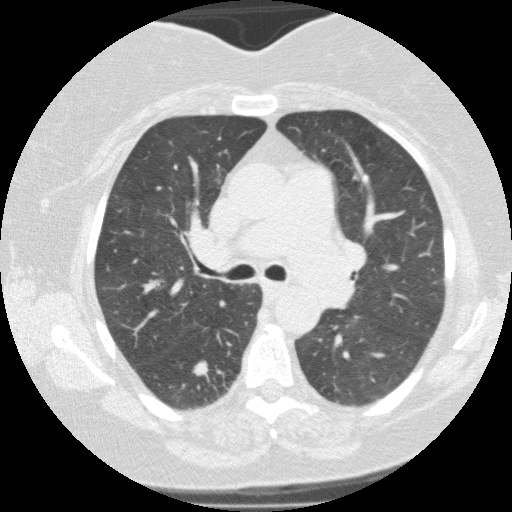
Low-dose screening chest CT, one axial slice. Slice 91 of 146 in the series (ordered by position). Lung window (W 1500 / L -600 HU). 2 mm slice thickness. 512 × 512 image matrix, field of view 330 × 330 mm.
Annotated regions visible in this slice (manually delineated by an expert):
- lesion 3 (nodule, lower lobe of right lung): bounding box [x1, y1, x2, y2] px = [193, 360, 211, 377]